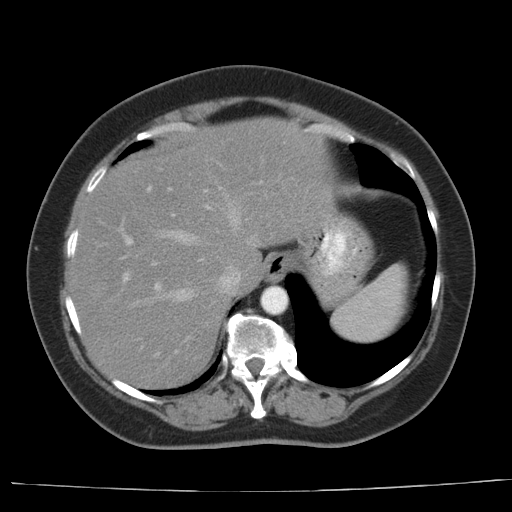
Contrast-enhanced abdominal CT, one axial slice; position 28 of 44 along the scan axis; 140 kVp; soft-tissue window (W 400 / L 40 HU); 5 mm slice thickness; 512 × 512 image matrix, field of view 373 × 373 mm. Female patient. Case-level facts recorded for this patient, not image findings: diagnosis: colorectal cancer liver metastases, imaged before liver resection.
Annotated regions visible in this slice (outlined manually by an expert reader):
- hepatic veins: bounding box [x1, y1, x2, y2] px = [157, 202, 256, 301]
- liver: [69, 120, 332, 389]
- planned liver remnant (the part of the liver to remain after resection): [101, 119, 333, 287]
- portal vein (with intrahepatic branches): [119, 180, 263, 353]